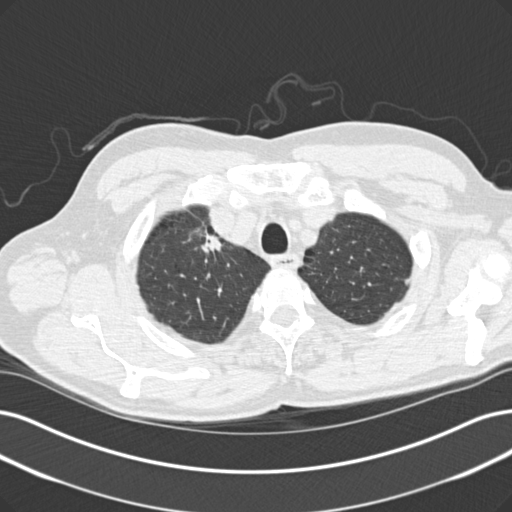
Low-dose screening chest CT, one axial slice; lung window (W 1500 / L -600 HU); 512 × 512 image matrix, field of view 365 × 365 mm.
Structures marked on this image (outlined manually by an expert reader):
- lesion 1 (tumor, upper lobe of right lung): box from (x=201, y=230) to (x=222, y=253) px